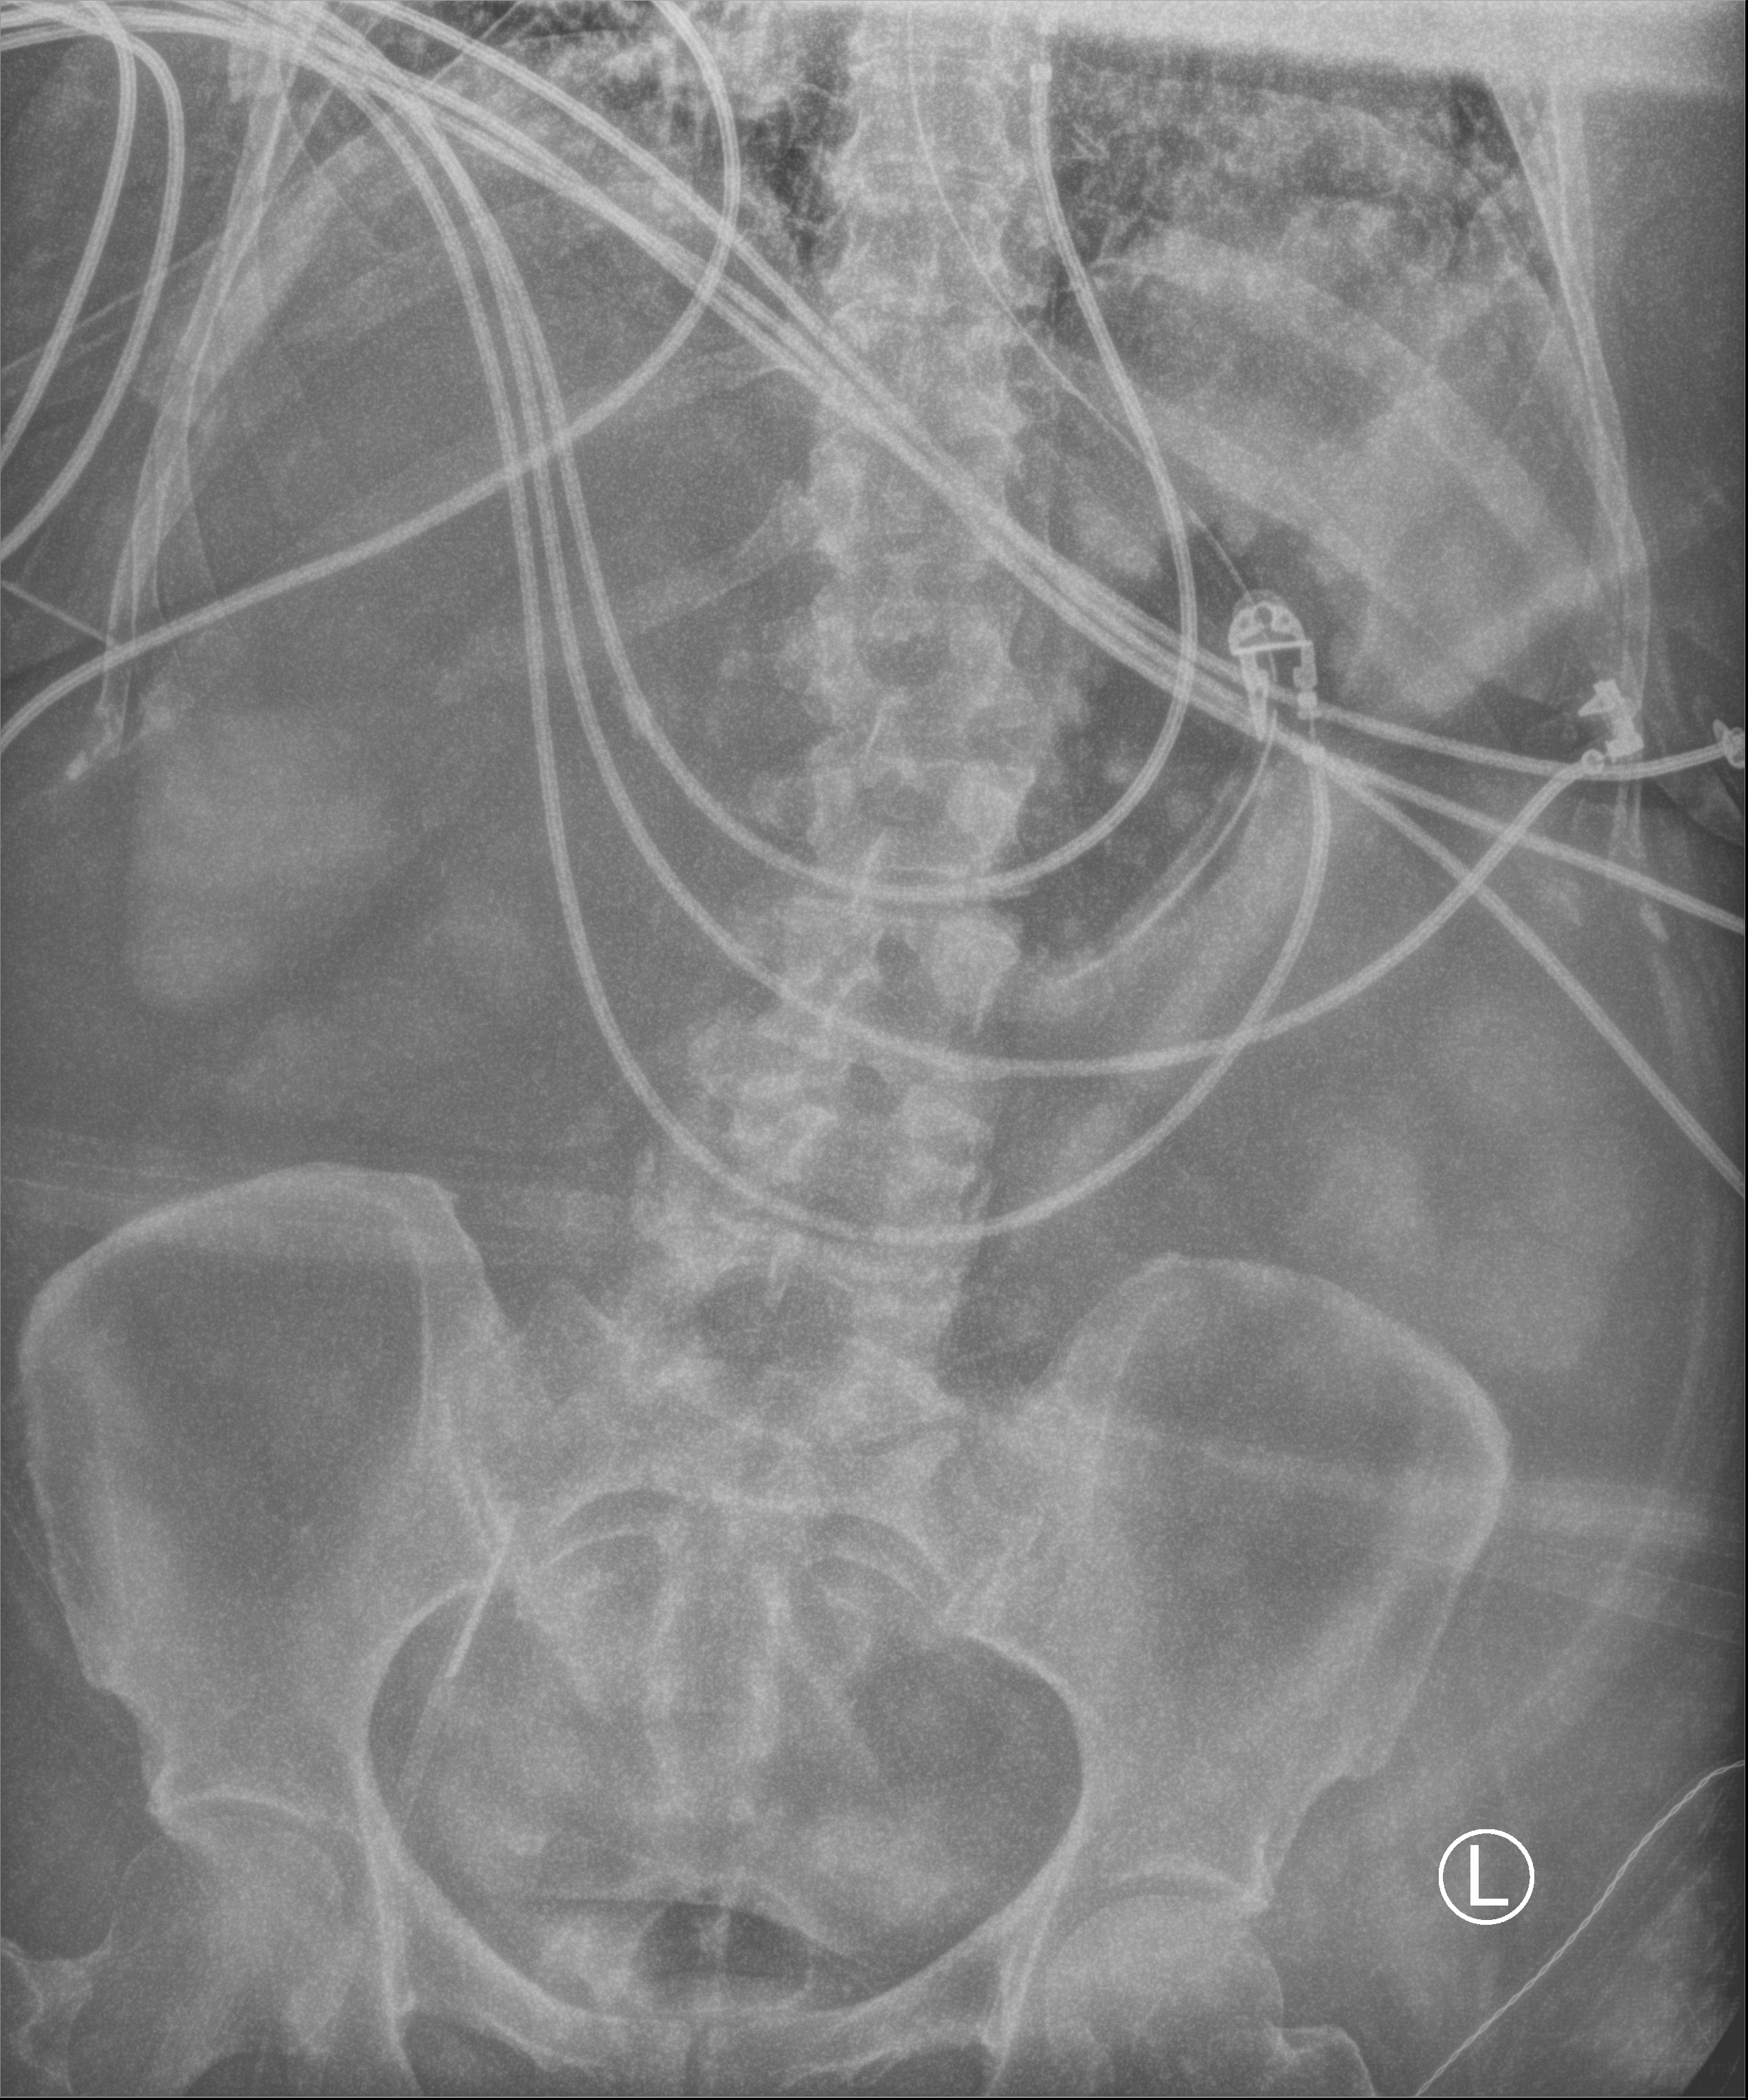
Bedside abdomen radiograph (computed radiography), anteroposterior (AP) projection. Female patient hospitalised with COVID-19, age 60–74 years.
From the hospital-stay record, not from the radiograph (when in the stay this image was taken is not recorded): mechanically ventilated during this hospital stay: yes; admitted to intensive care during this hospital stay: yes; length of hospital stay: 45 days.